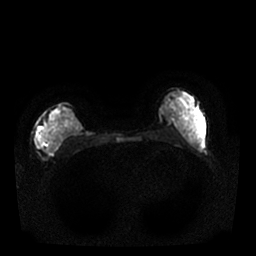
Breast MRI, one axial slice; slice 11 of 25 in the series (ordered by position); diffusion-weighted series; image 2 of 4 stored at this slice position (different b-values; order by instance number); 1.5 T; 4 mm slice thickness; 256 × 256 image matrix, field of view 340 × 340 mm. Female patient.
Annotated regions visible in this slice (manually delineated by an expert):
- tumour on diffusion-weighted imaging: bounding box [x1, y1, x2, y2] px = [38, 126, 57, 151]